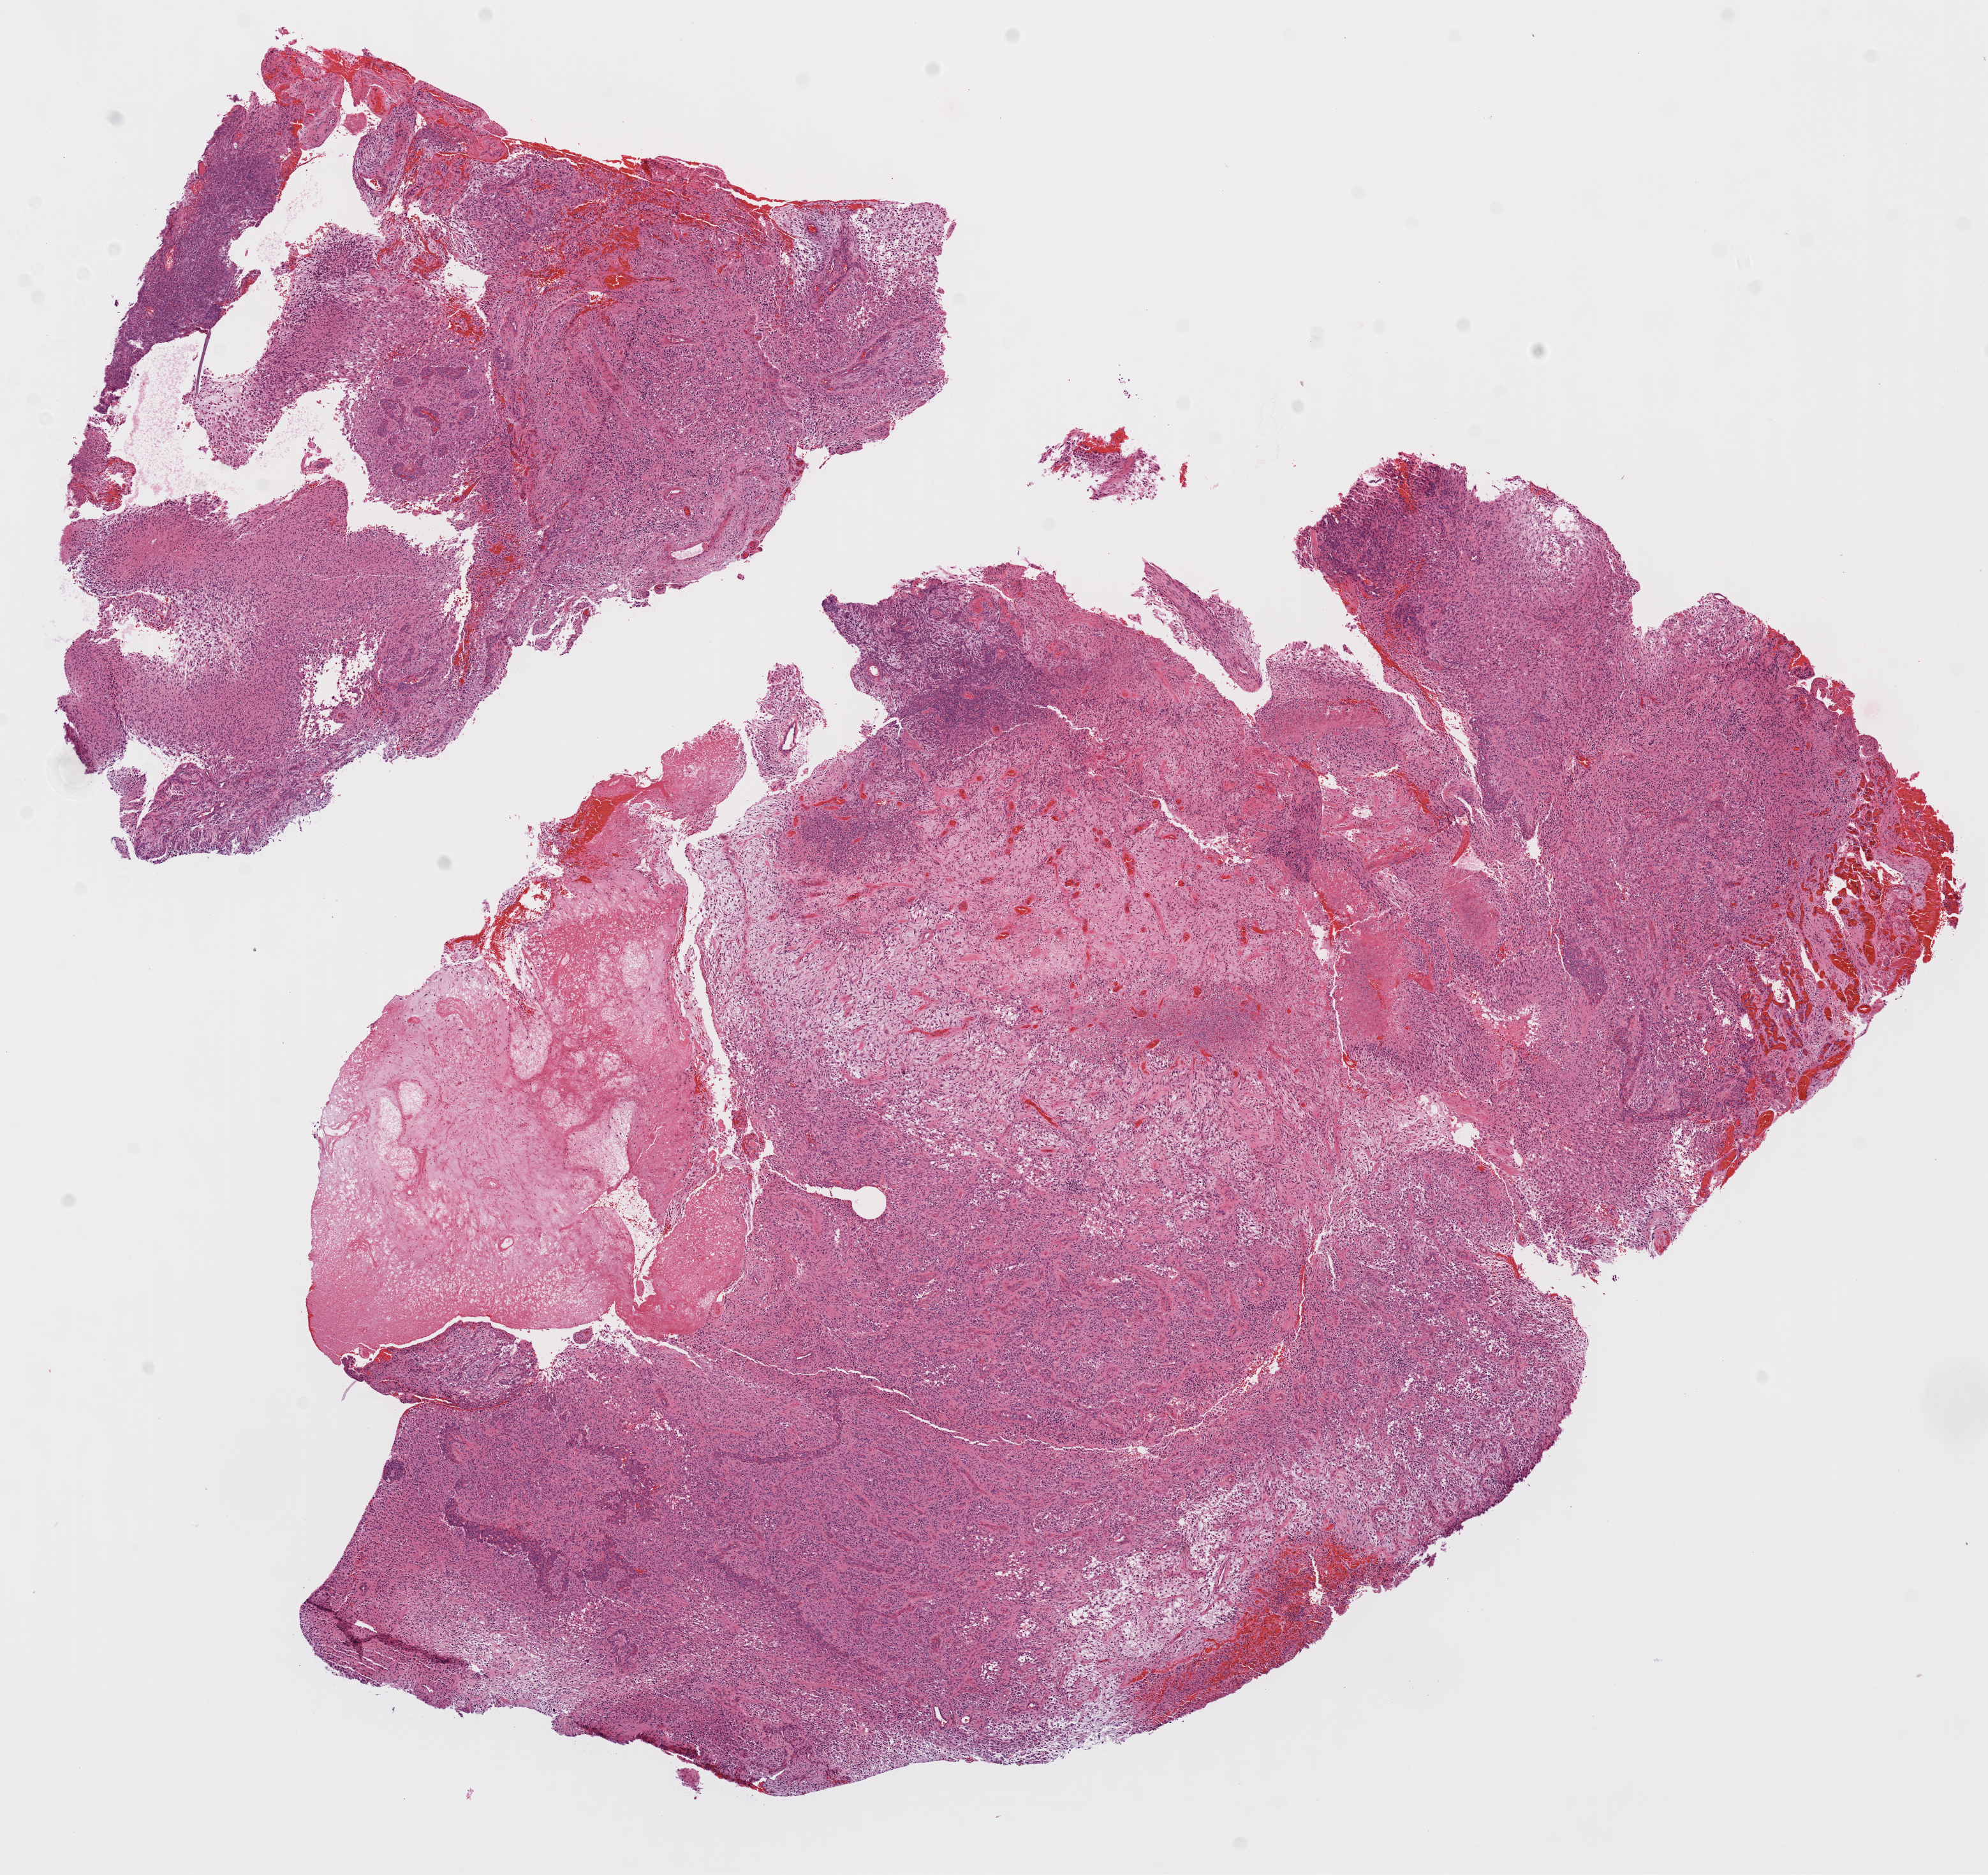
H&E-stained whole-slide image, low-resolution overview of the scanned area, about 12.6 x 11.9 mm, formalin-fixed paraffin-embedded (FFPE) diagnostic section, sample: primary tumour, brain. Patient: male, age at initial diagnosis 67 years.
Histologic diagnosis: Glioblastoma.